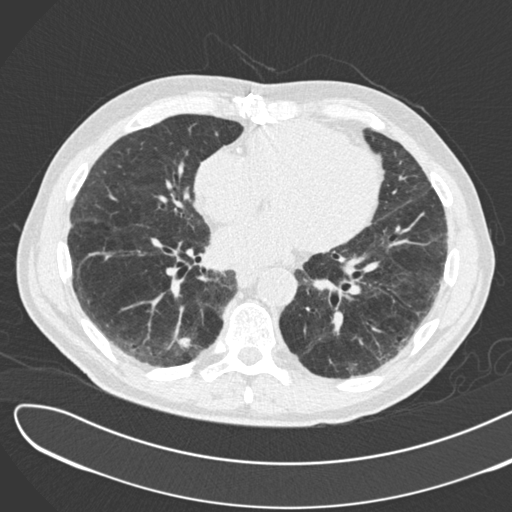
Axial slice from a low-dose chest CT screening exam; second screening round (one year after baseline); lung window (W 1500 / L -600 HU); 2 mm slice thickness; standard (soft-tissue) reconstruction kernel (B30f); slice 111 of 183 in the series. Male participant, aged 72 years at enrolment. Former smoker at enrolment.
Expert reader's lesion annotation, bounding box [x1, y1, x2, y2] px = [165, 325, 206, 359]. The screening reader recorded 2 non-calcified nodules or masses ≥4 mm on this exam; which of them this box marks is not recorded. Lung cancer was diagnosed 46 days after this screen: squamous cell carcinoma, NOS, right lower lobe, poorly differentiated (G3), stage IB (AJCC 6th edition), 42 mm at pathology.